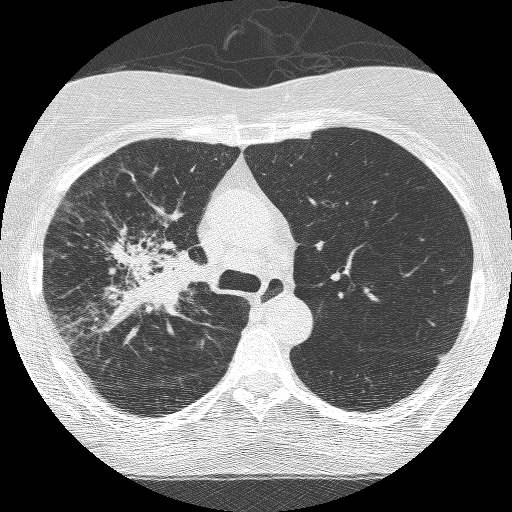
Low-dose screening chest CT, axial slice, third annual screen, lung window (W 1500 / L -600 HU), slice 176 of 253 in the series, 512 × 512 image matrix, field of view 294 × 294 mm. Female participant, aged 64 years at enrolment. Former smoker at enrolment.
Lesion marked by an expert reader, bounding box (x1, y1, x2, y2) in pixels: (91, 222, 206, 337). Reader record for this screening exam (exam-level; its link to the box is not recorded): non-calcified nodule or mass ≥4 mm, right upper lobe, 49 × 43 mm, spiculated (stellate) margins, soft tissue attenuation, pre-existing on the prior screen: yes; interval growth: yes. Official screen result: positive, other. Participant outcome: lung cancer diagnosed 7 days after this screen — adenocarcinoma, NOS, right upper lobe, right middle lobe, right hilum, stage IV (AJCC 6th edition), 85 mm at pathology.